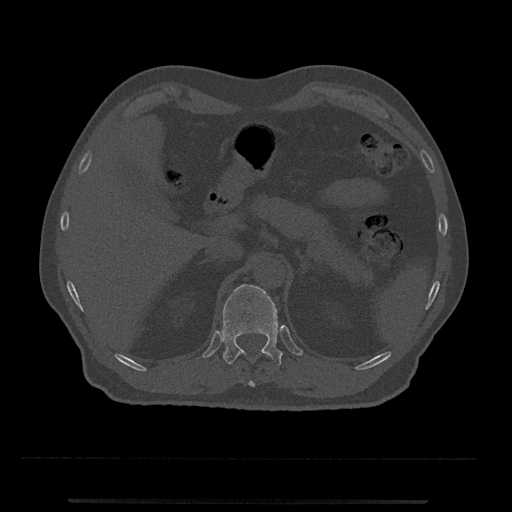
CT including the spine, one axial slice; slice 417 of 797 in the series (ordered by position); 120 kVp; bone window (W 1800 / L 400 HU); 0.5 mm slice thickness; 512 × 512 image matrix, field of view 419 × 419 mm. Male patient, age 63 years. Case-level facts recorded for this patient, not image findings: primary cancer: prostate.
Outlined on this slice (semi-automatically segmented with operator editing):
- T11 vertebra: bounding box [x1, y1, x2, y2] px = [238, 351, 270, 387]
- T12 vertebra: [223, 284, 283, 366]